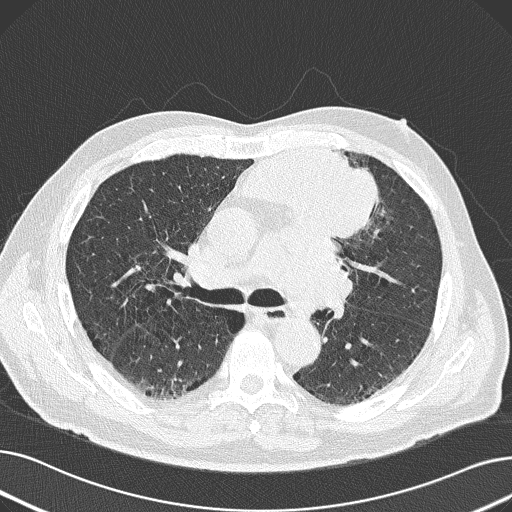
Low-dose screening chest CT, axial slice; baseline annual screen; lung window (W 1500 / L -600 HU); lung (sharp) reconstruction kernel (B50f); slice 72 of 165 in the series. Male, age 69 years at enrolment. Former smoker at enrolment.
Expert-annotated lung lesion, bounding box [x1, y1, x2, y2] px = [234, 135, 383, 250]. Screening reader's record for this exam (one nodule recorded; not confirmed to be the boxed lesion): non-calcified nodule or mass ≥4 mm, left upper lobe, 6 × 10 mm, spiculated (stellate) margins, soft tissue attenuation. Participant outcome: lung cancer diagnosed 20 days after this screen — non-small cell carcinoma, left upper lobe, poorly differentiated (G3), stage IB (AJCC 6th edition), 100 mm at pathology.